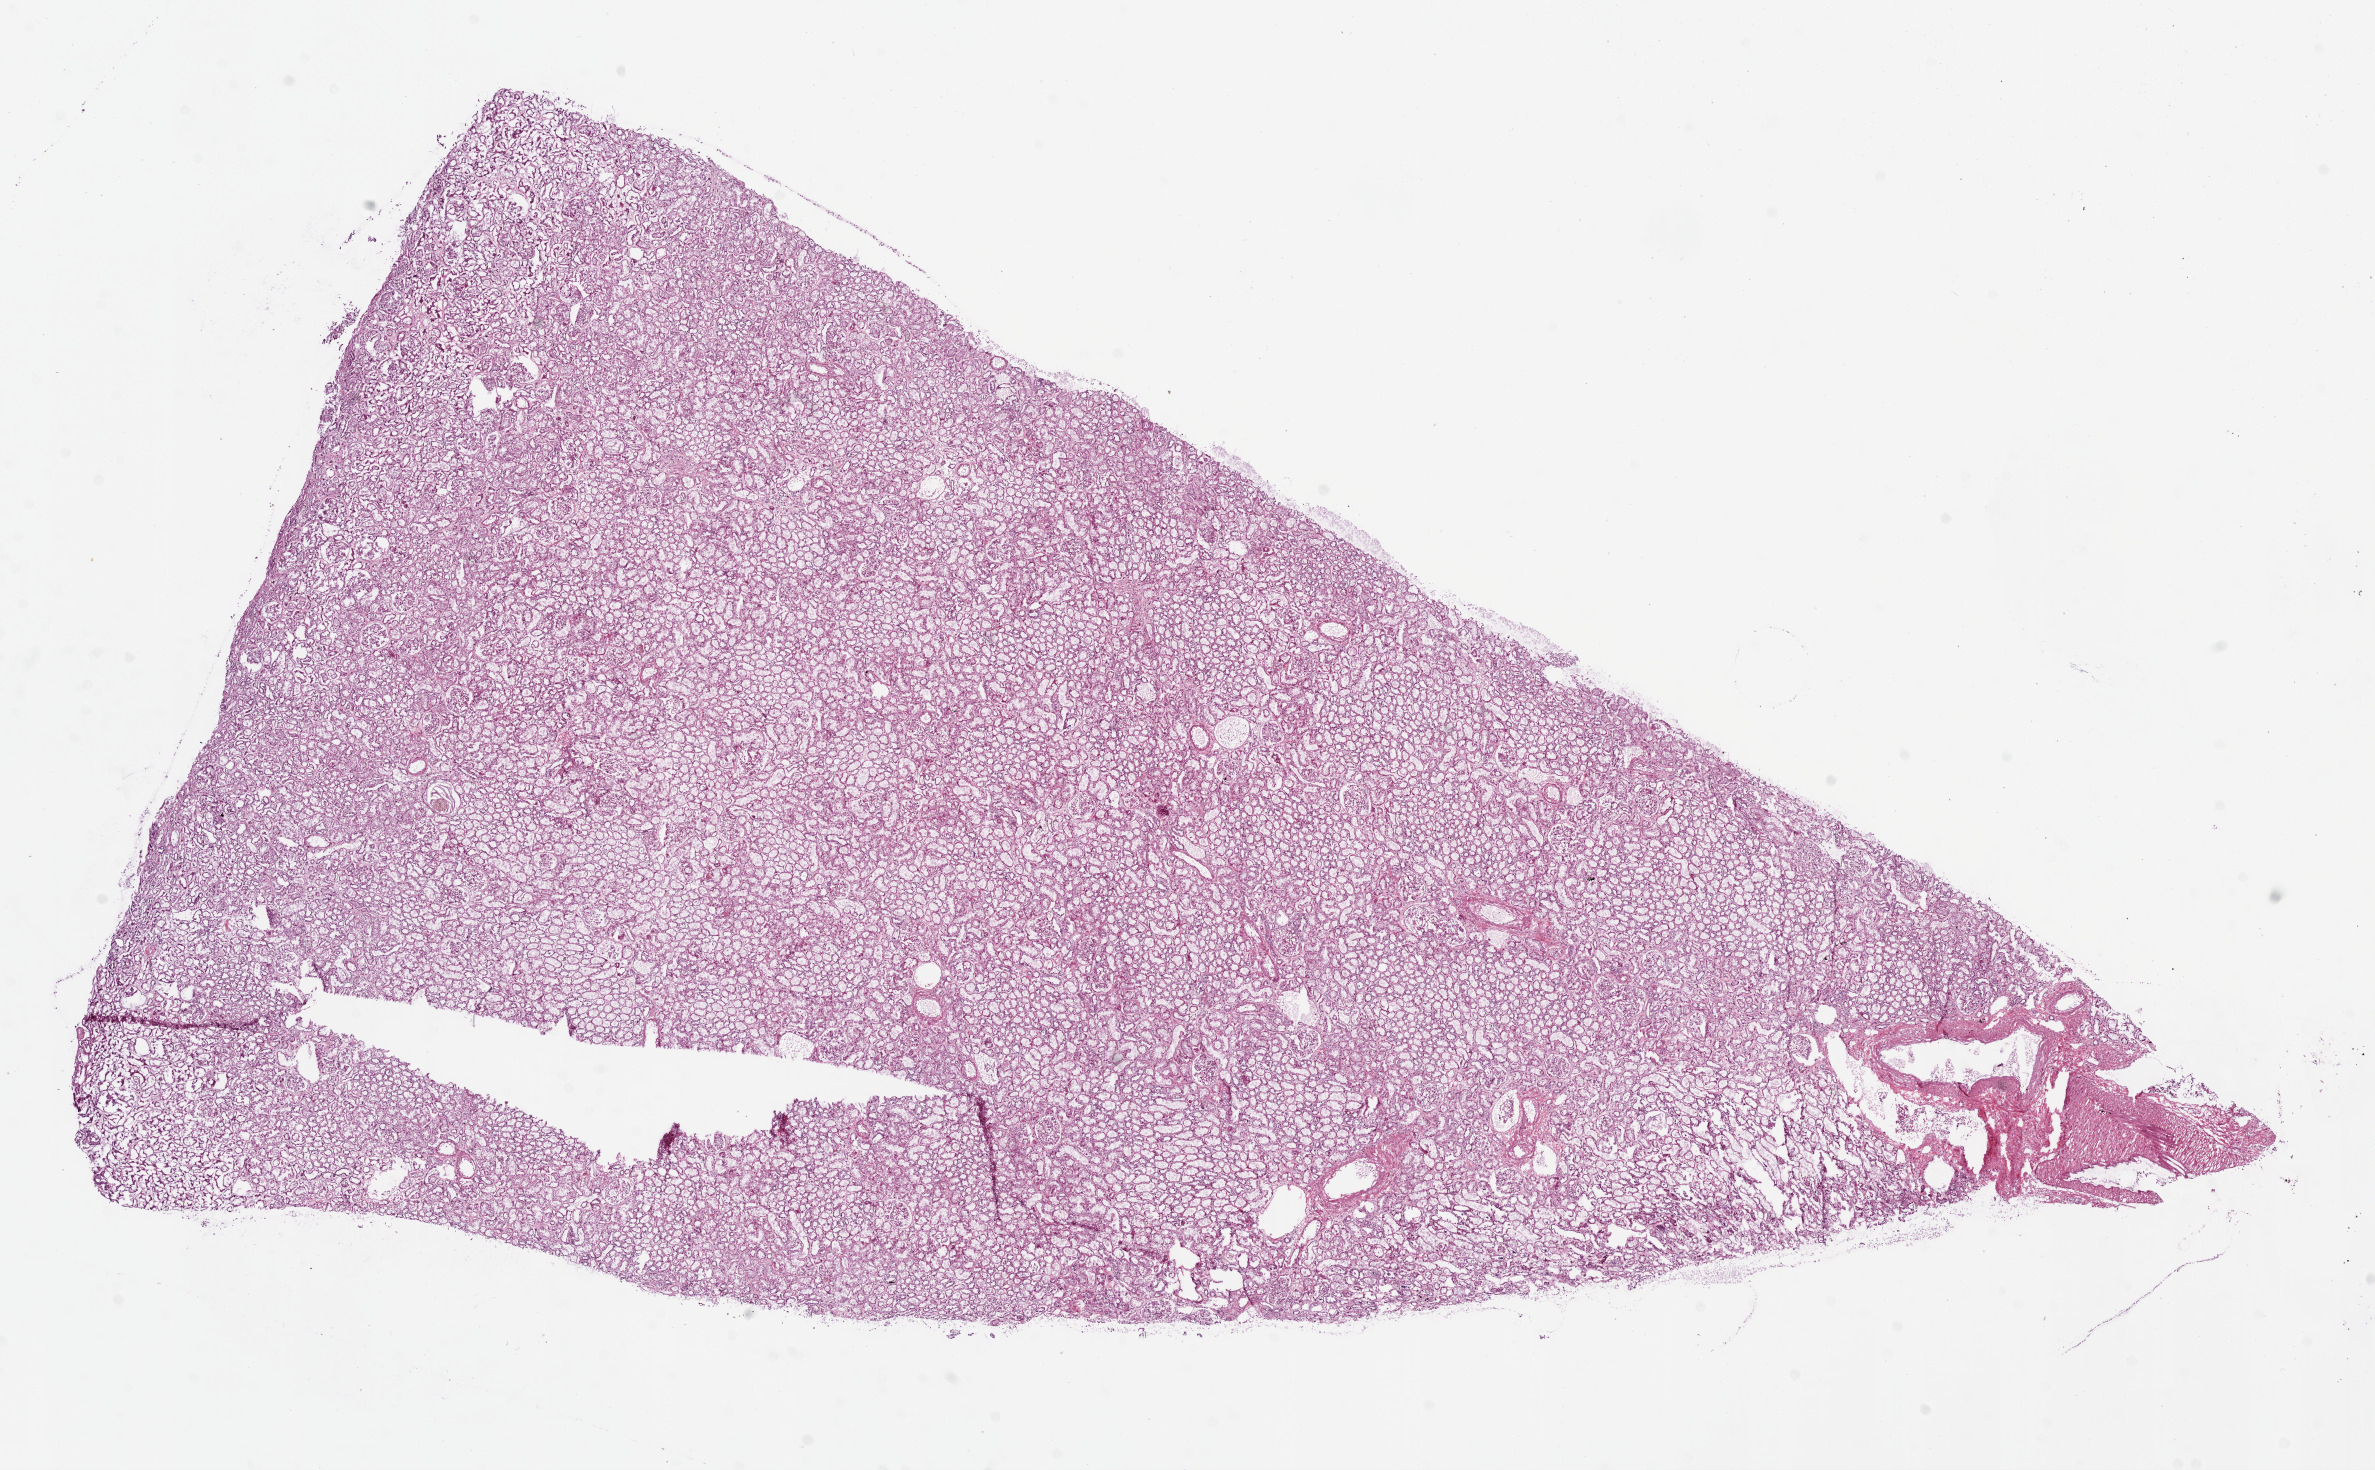
Hematoxylin and eosin (H&E) stained whole-slide image — low-resolution overview of the scanned area, about 19.1 x 11.8 mm (acquisition: 20x scan), frozen section from the bottom of the tissue portion, sample: solid tissue normal (non-tumour tissue), kidney. Male patient; age at initial diagnosis 58 years.
• this section: solid tissue normal sample (biorepository sample class)
• patient diagnosis: Clear cell adenocarcinoma, NOS